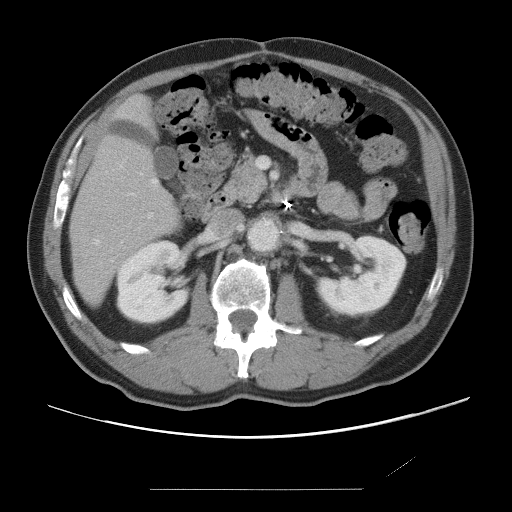
Contrast-enhanced abdominal CT, one axial slice. Slice 29 of 87 in the series (ordered by position). 120 kVp. Intravenous contrast given. Soft-tissue window (W 400 / L 40 HU). 5 mm slice thickness. 512 × 512 image matrix. Male patient, age 74 years. From the clinical record (not read from this slice): diagnosis: colorectal cancer liver metastases, imaged before liver resection; multiple liver metastases: yes; largest metastasis: 1.1 cm; chemotherapy before resection: yes.
Outlined on this slice (outlined manually by an expert reader):
- hepatic veins: box from (x=94, y=179) to (x=157, y=244) px
- liver: (x=70, y=99)–(x=179, y=304)
- planned liver remnant (the part of the liver to remain after resection): (x=70, y=99)–(x=179, y=303)
- portal vein (with intrahepatic branches): (x=140, y=173)–(x=153, y=218)
- liver metastasis: (x=77, y=255)–(x=83, y=266)